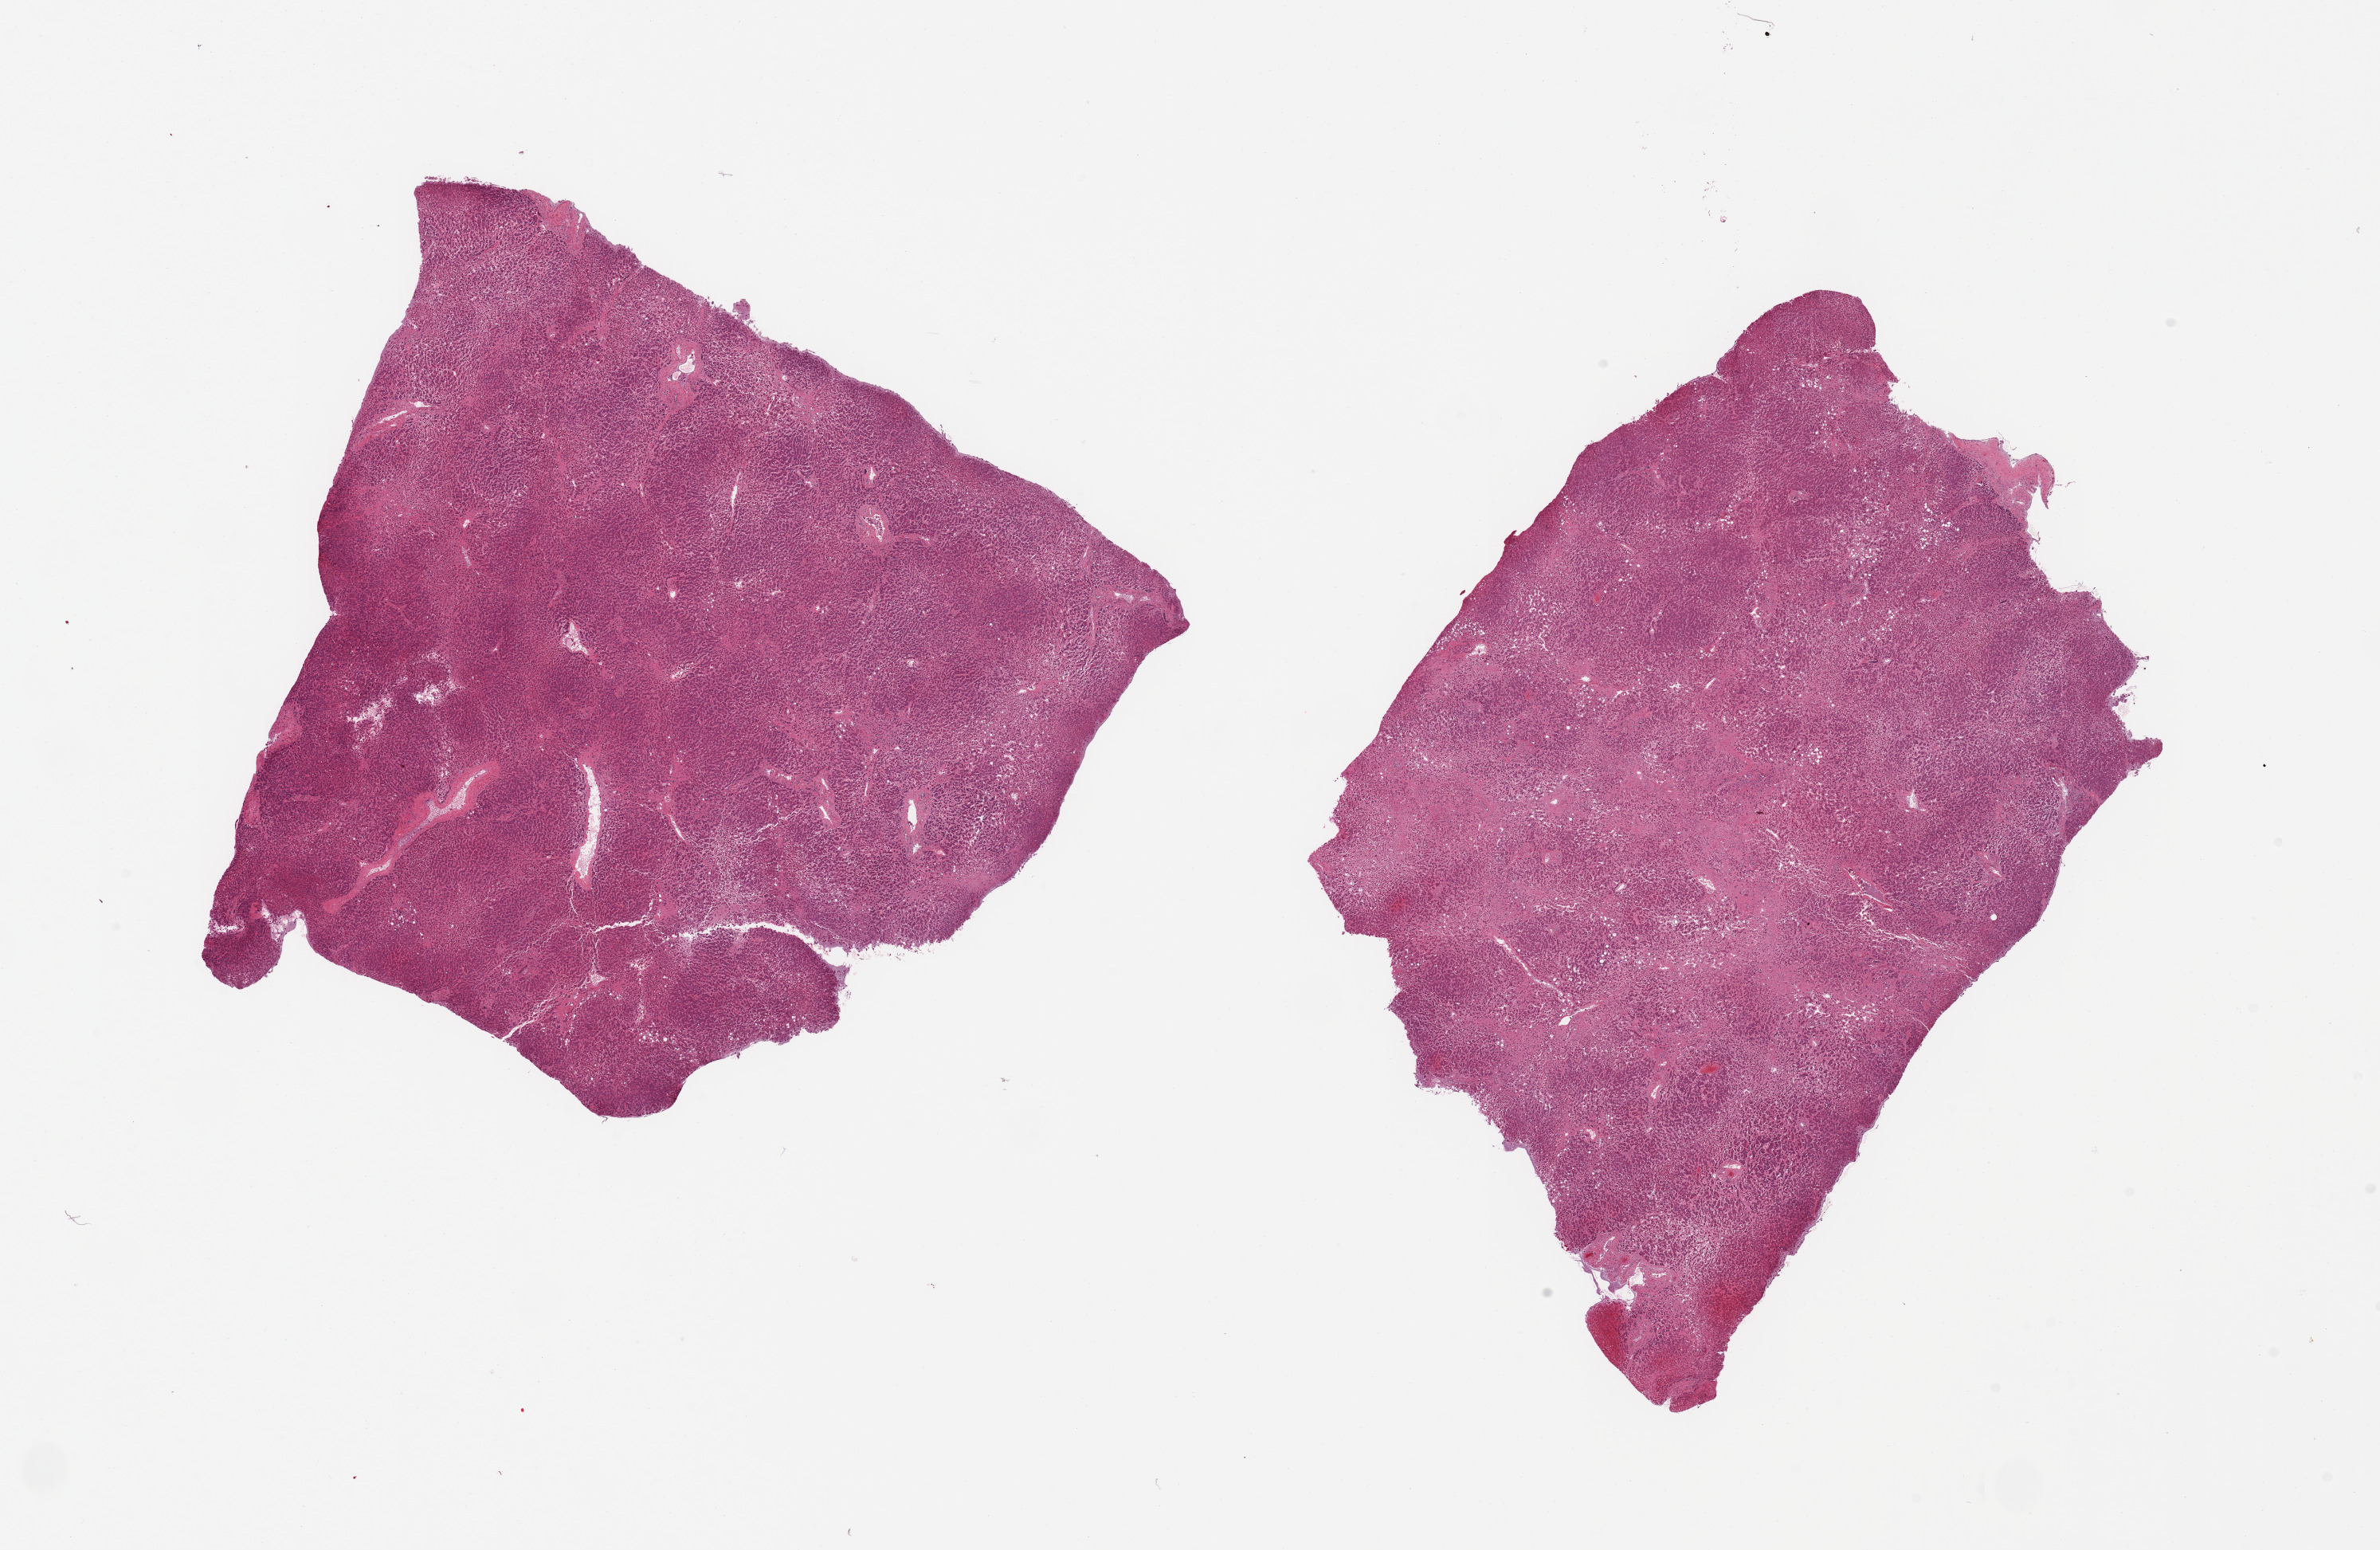
Whole-slide image, H&E stain, brightfield, low-resolution overview of the scanned area, about 23.6 x 15.4 mm. Donor: male.
Specimen: PAXgene-fixed, paraffin-embedded tissue; section of liver (target tissue); donor tissue sample.